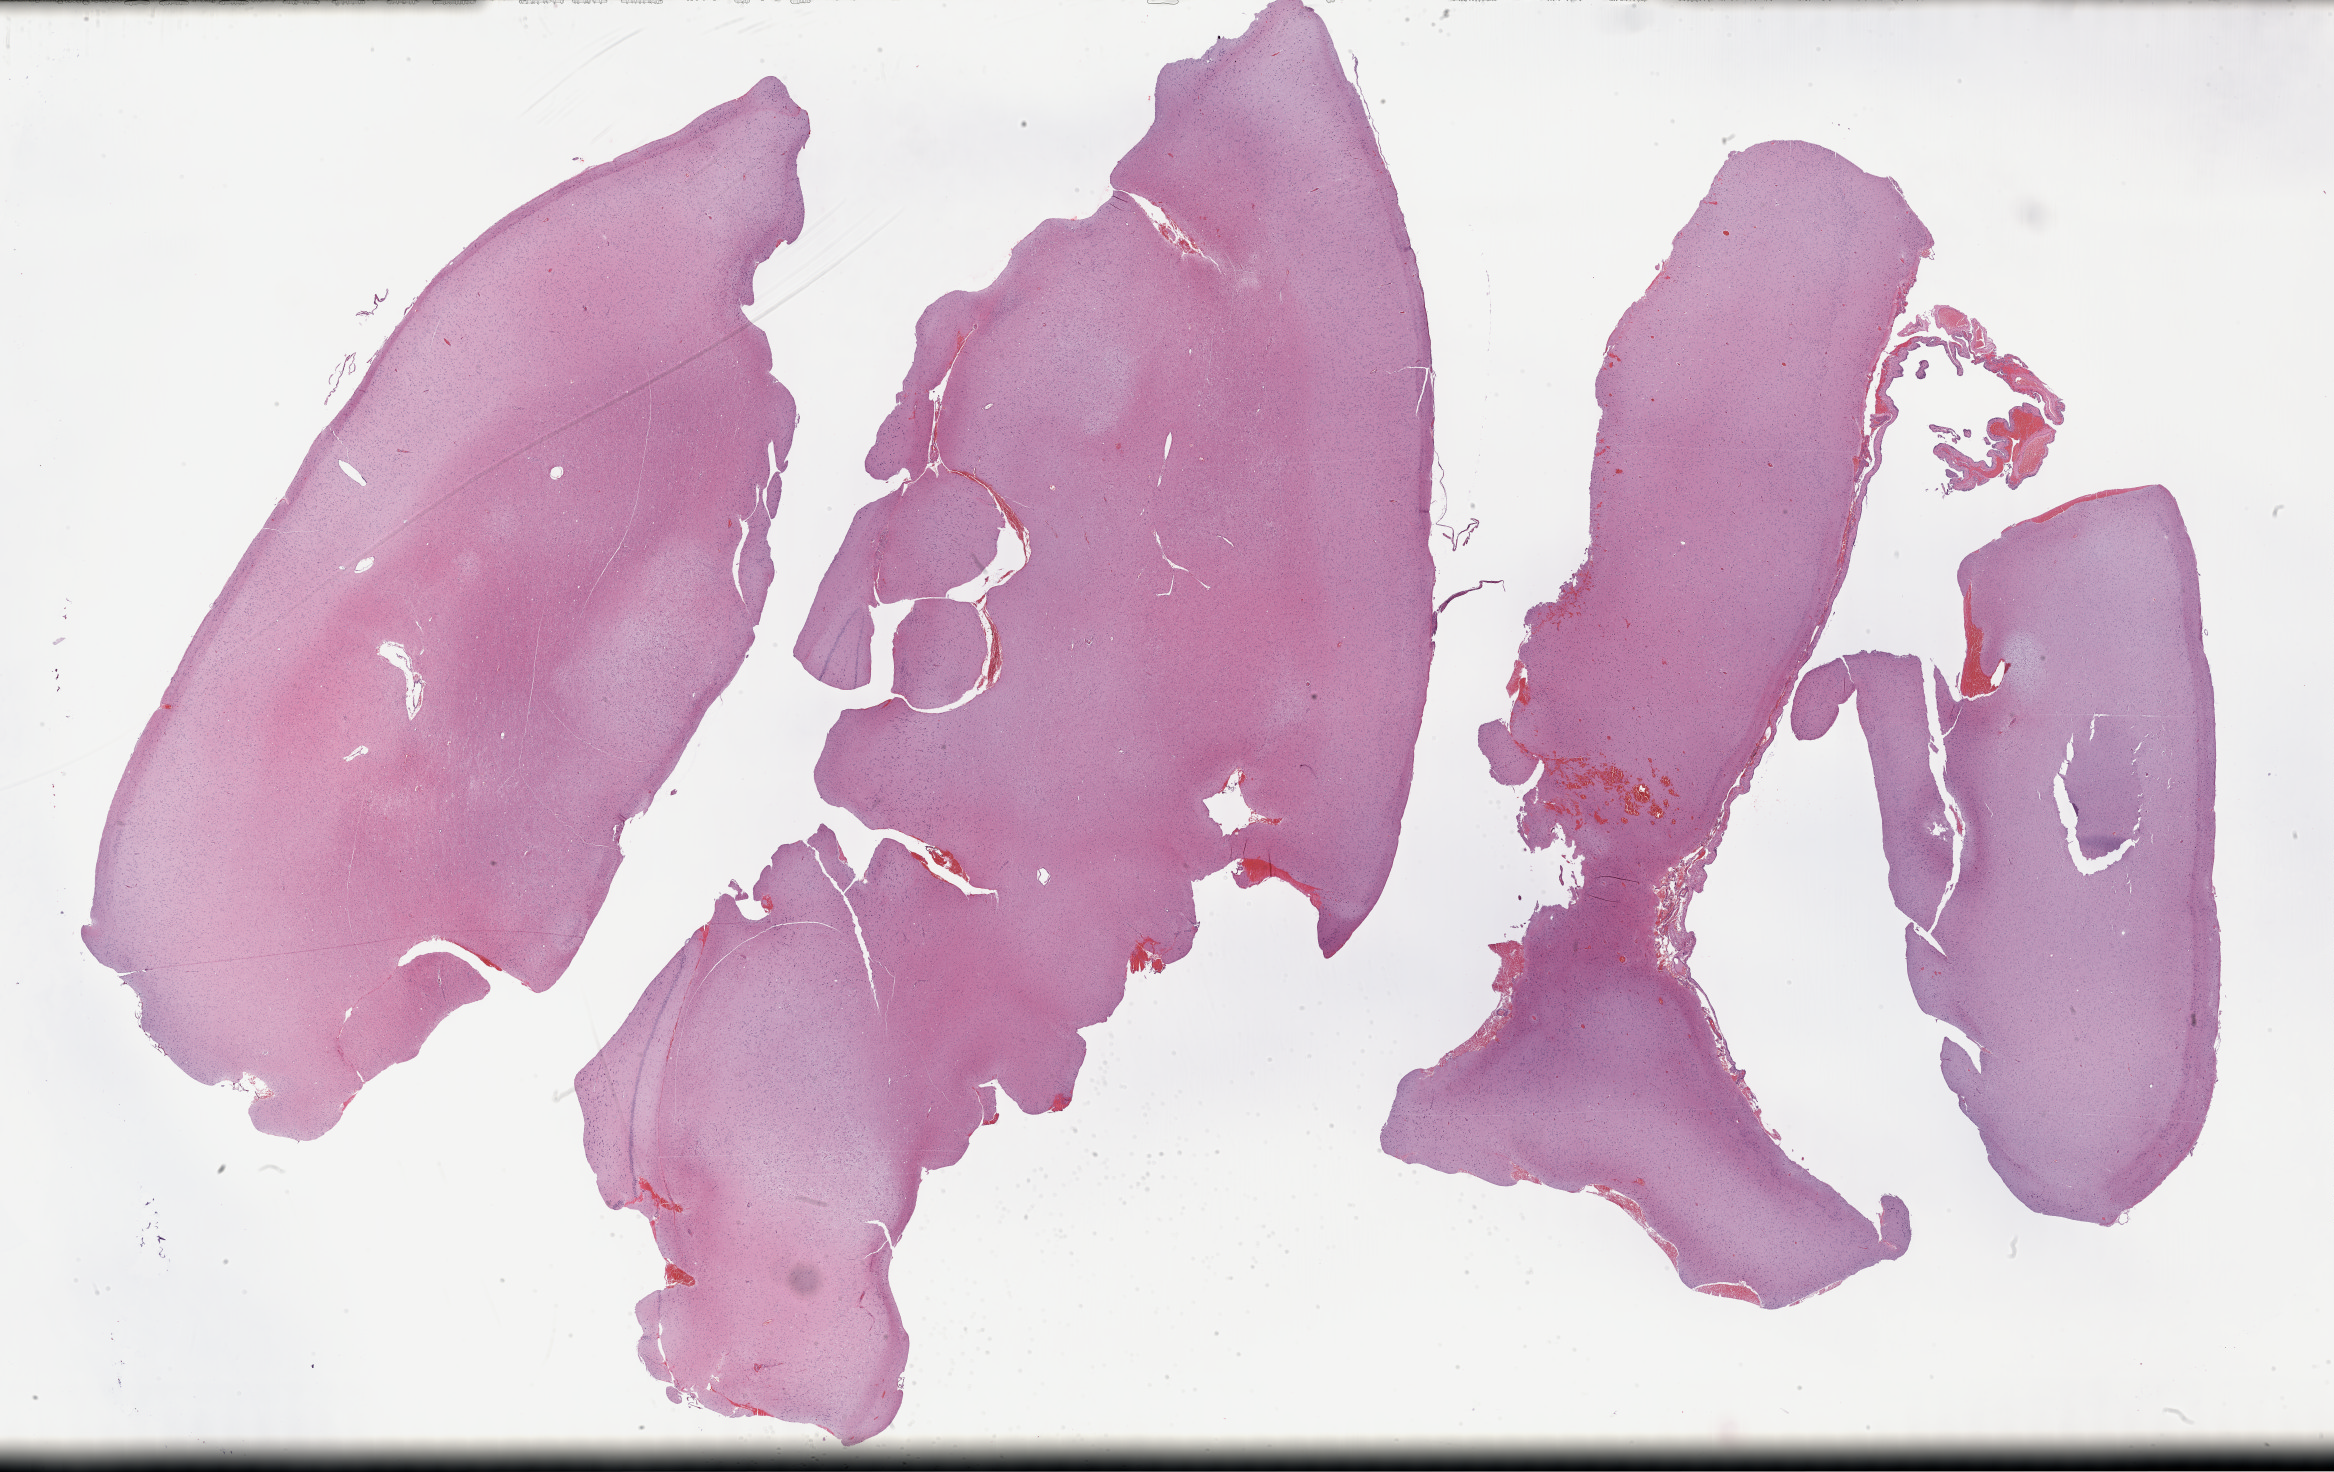
Whole-slide histology image, Hematoxylin and eosin (H&E) stained — a low-resolution overview of the entire scanned area, about 37.8 x 23.8 mm (from a 40x scan). Formalin-fixed paraffin-embedded (FFPE) diagnostic section. Primary tumour sample from the brain. Female patient; age at initial diagnosis 37 years. Histologic grade: G2 (moderately differentiated).
• laterality: left
• diagnosis: Astrocytoma, NOS (cerebrum)